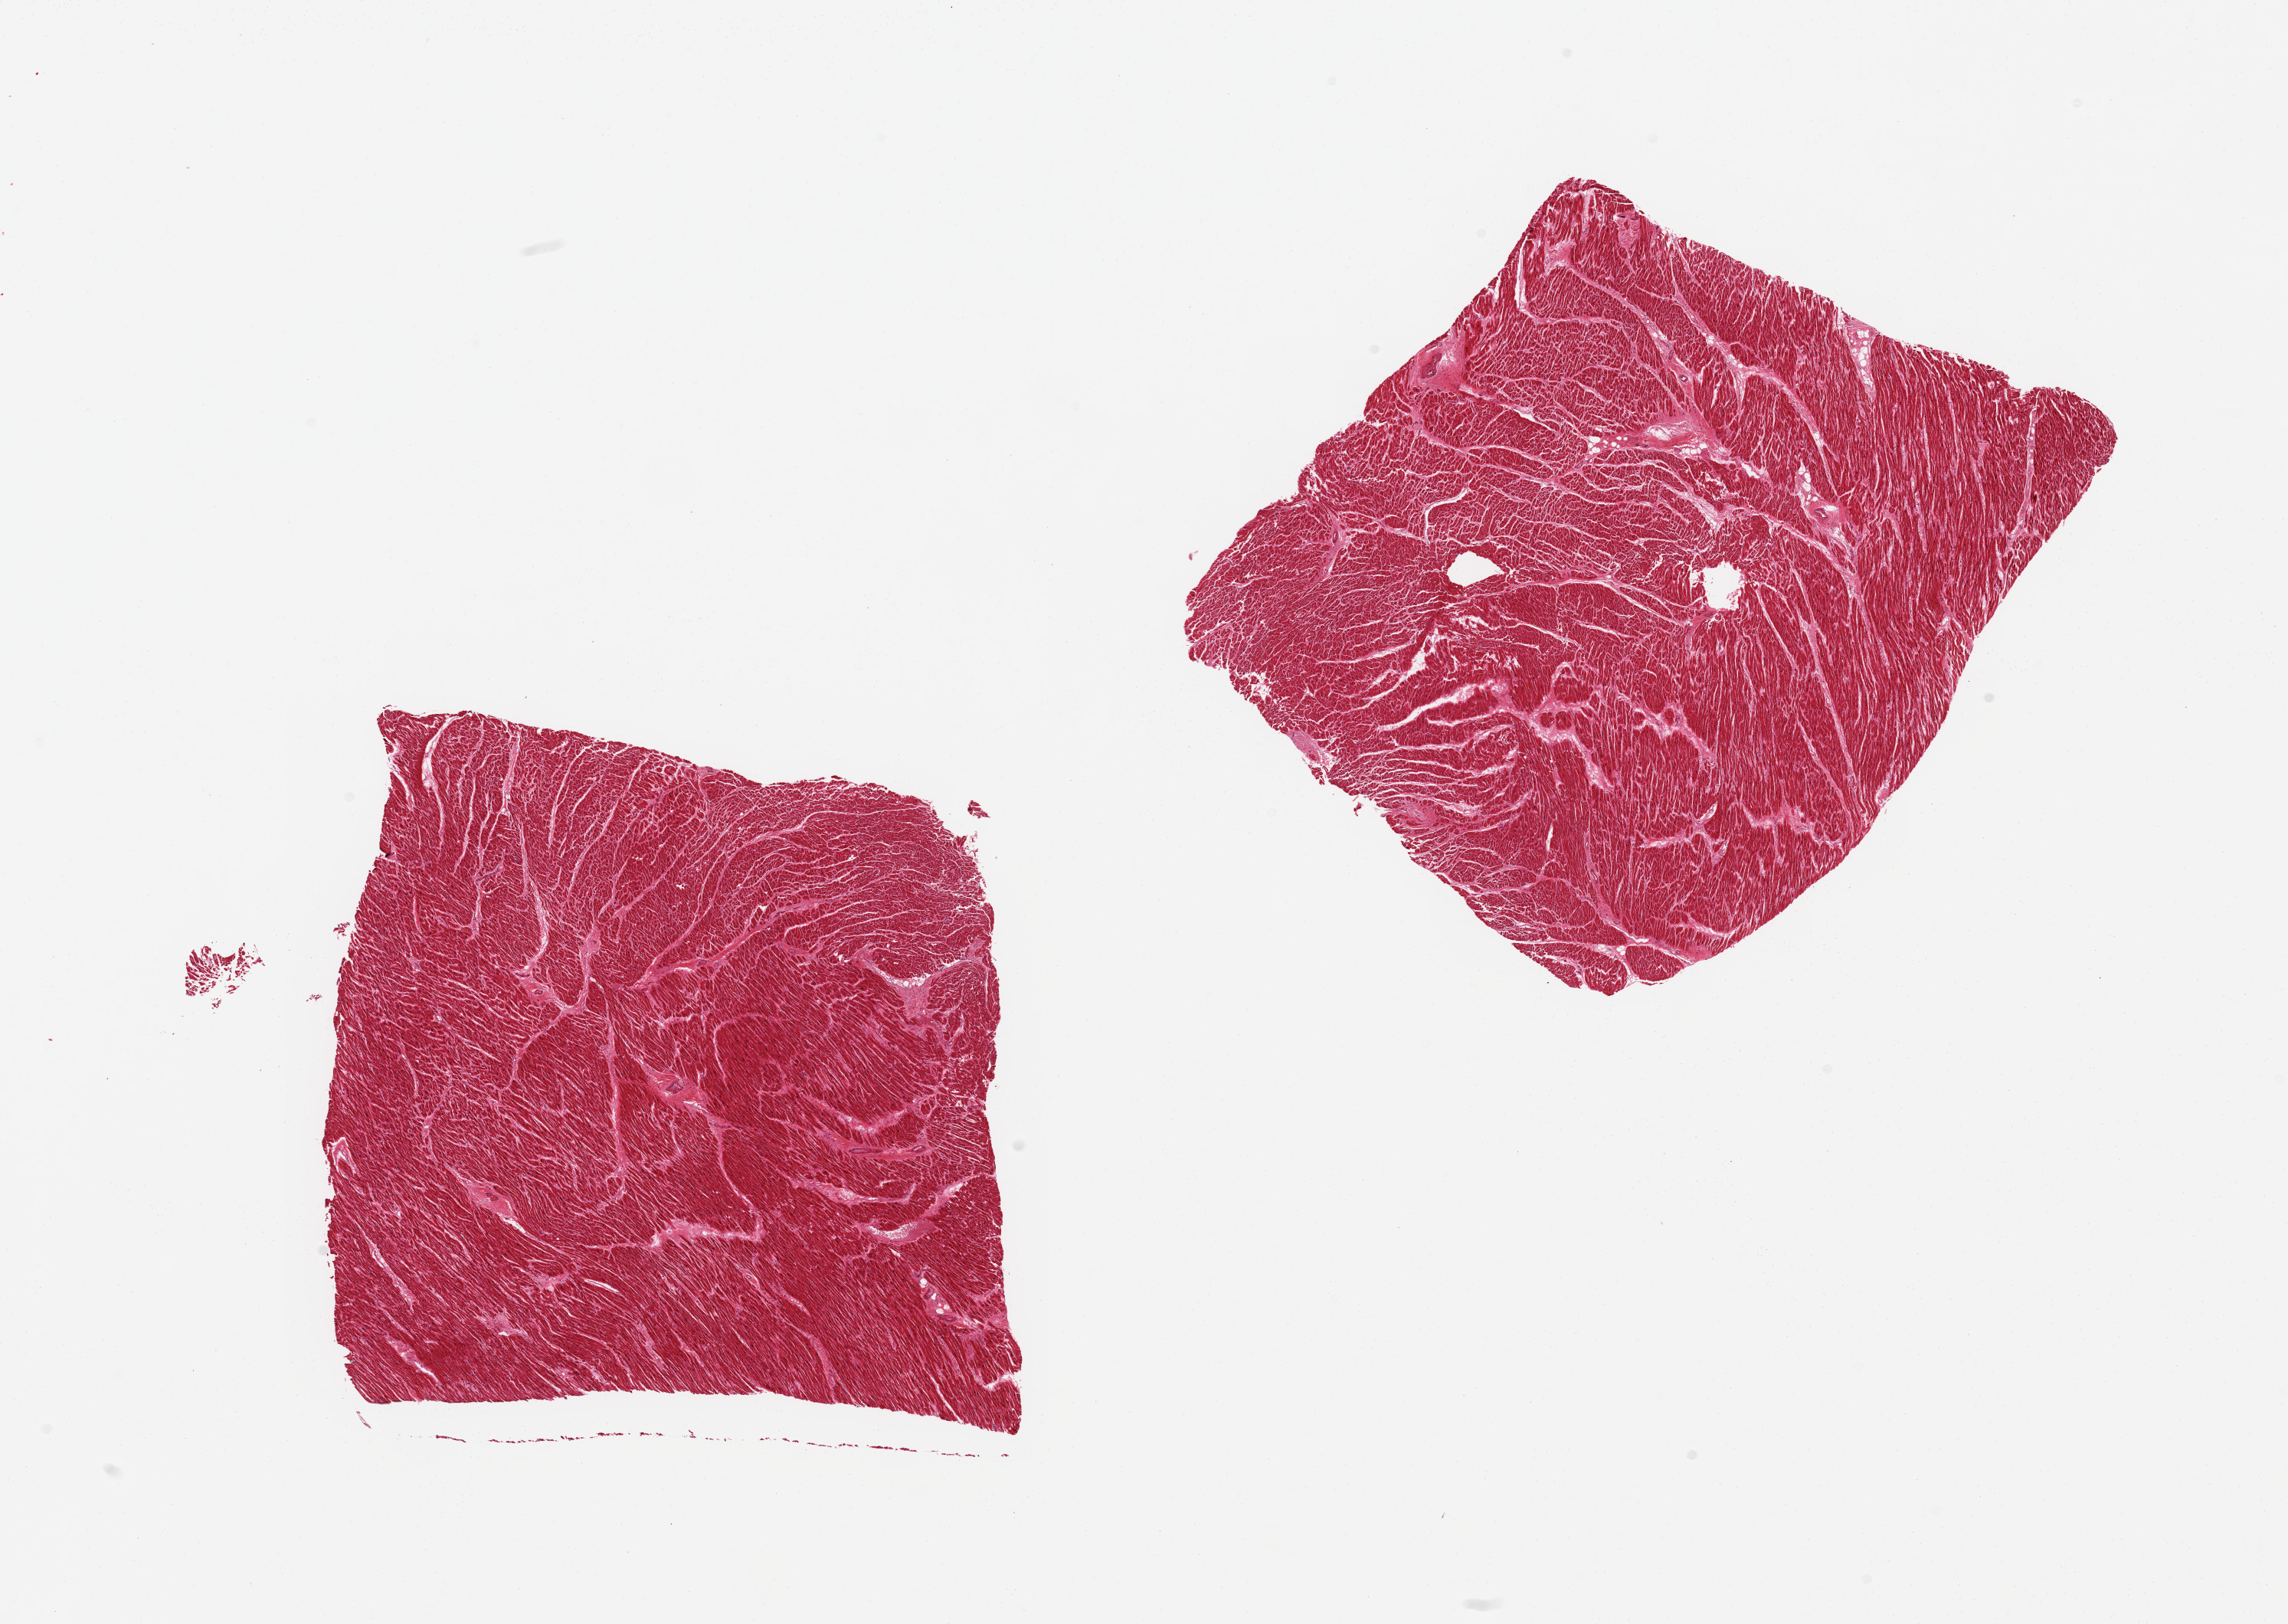
Digitized hematoxylin and eosin (H&E)-stained section, brightfield — whole scanned area (about 23.6 x 16.8 mm) shown as a low-resolution overview; PAXgene-fixed, paraffin-embedded tissue; target tissue: heart; tissue donor sample.
• reviewer comment on this tissue sample: 2 pieces